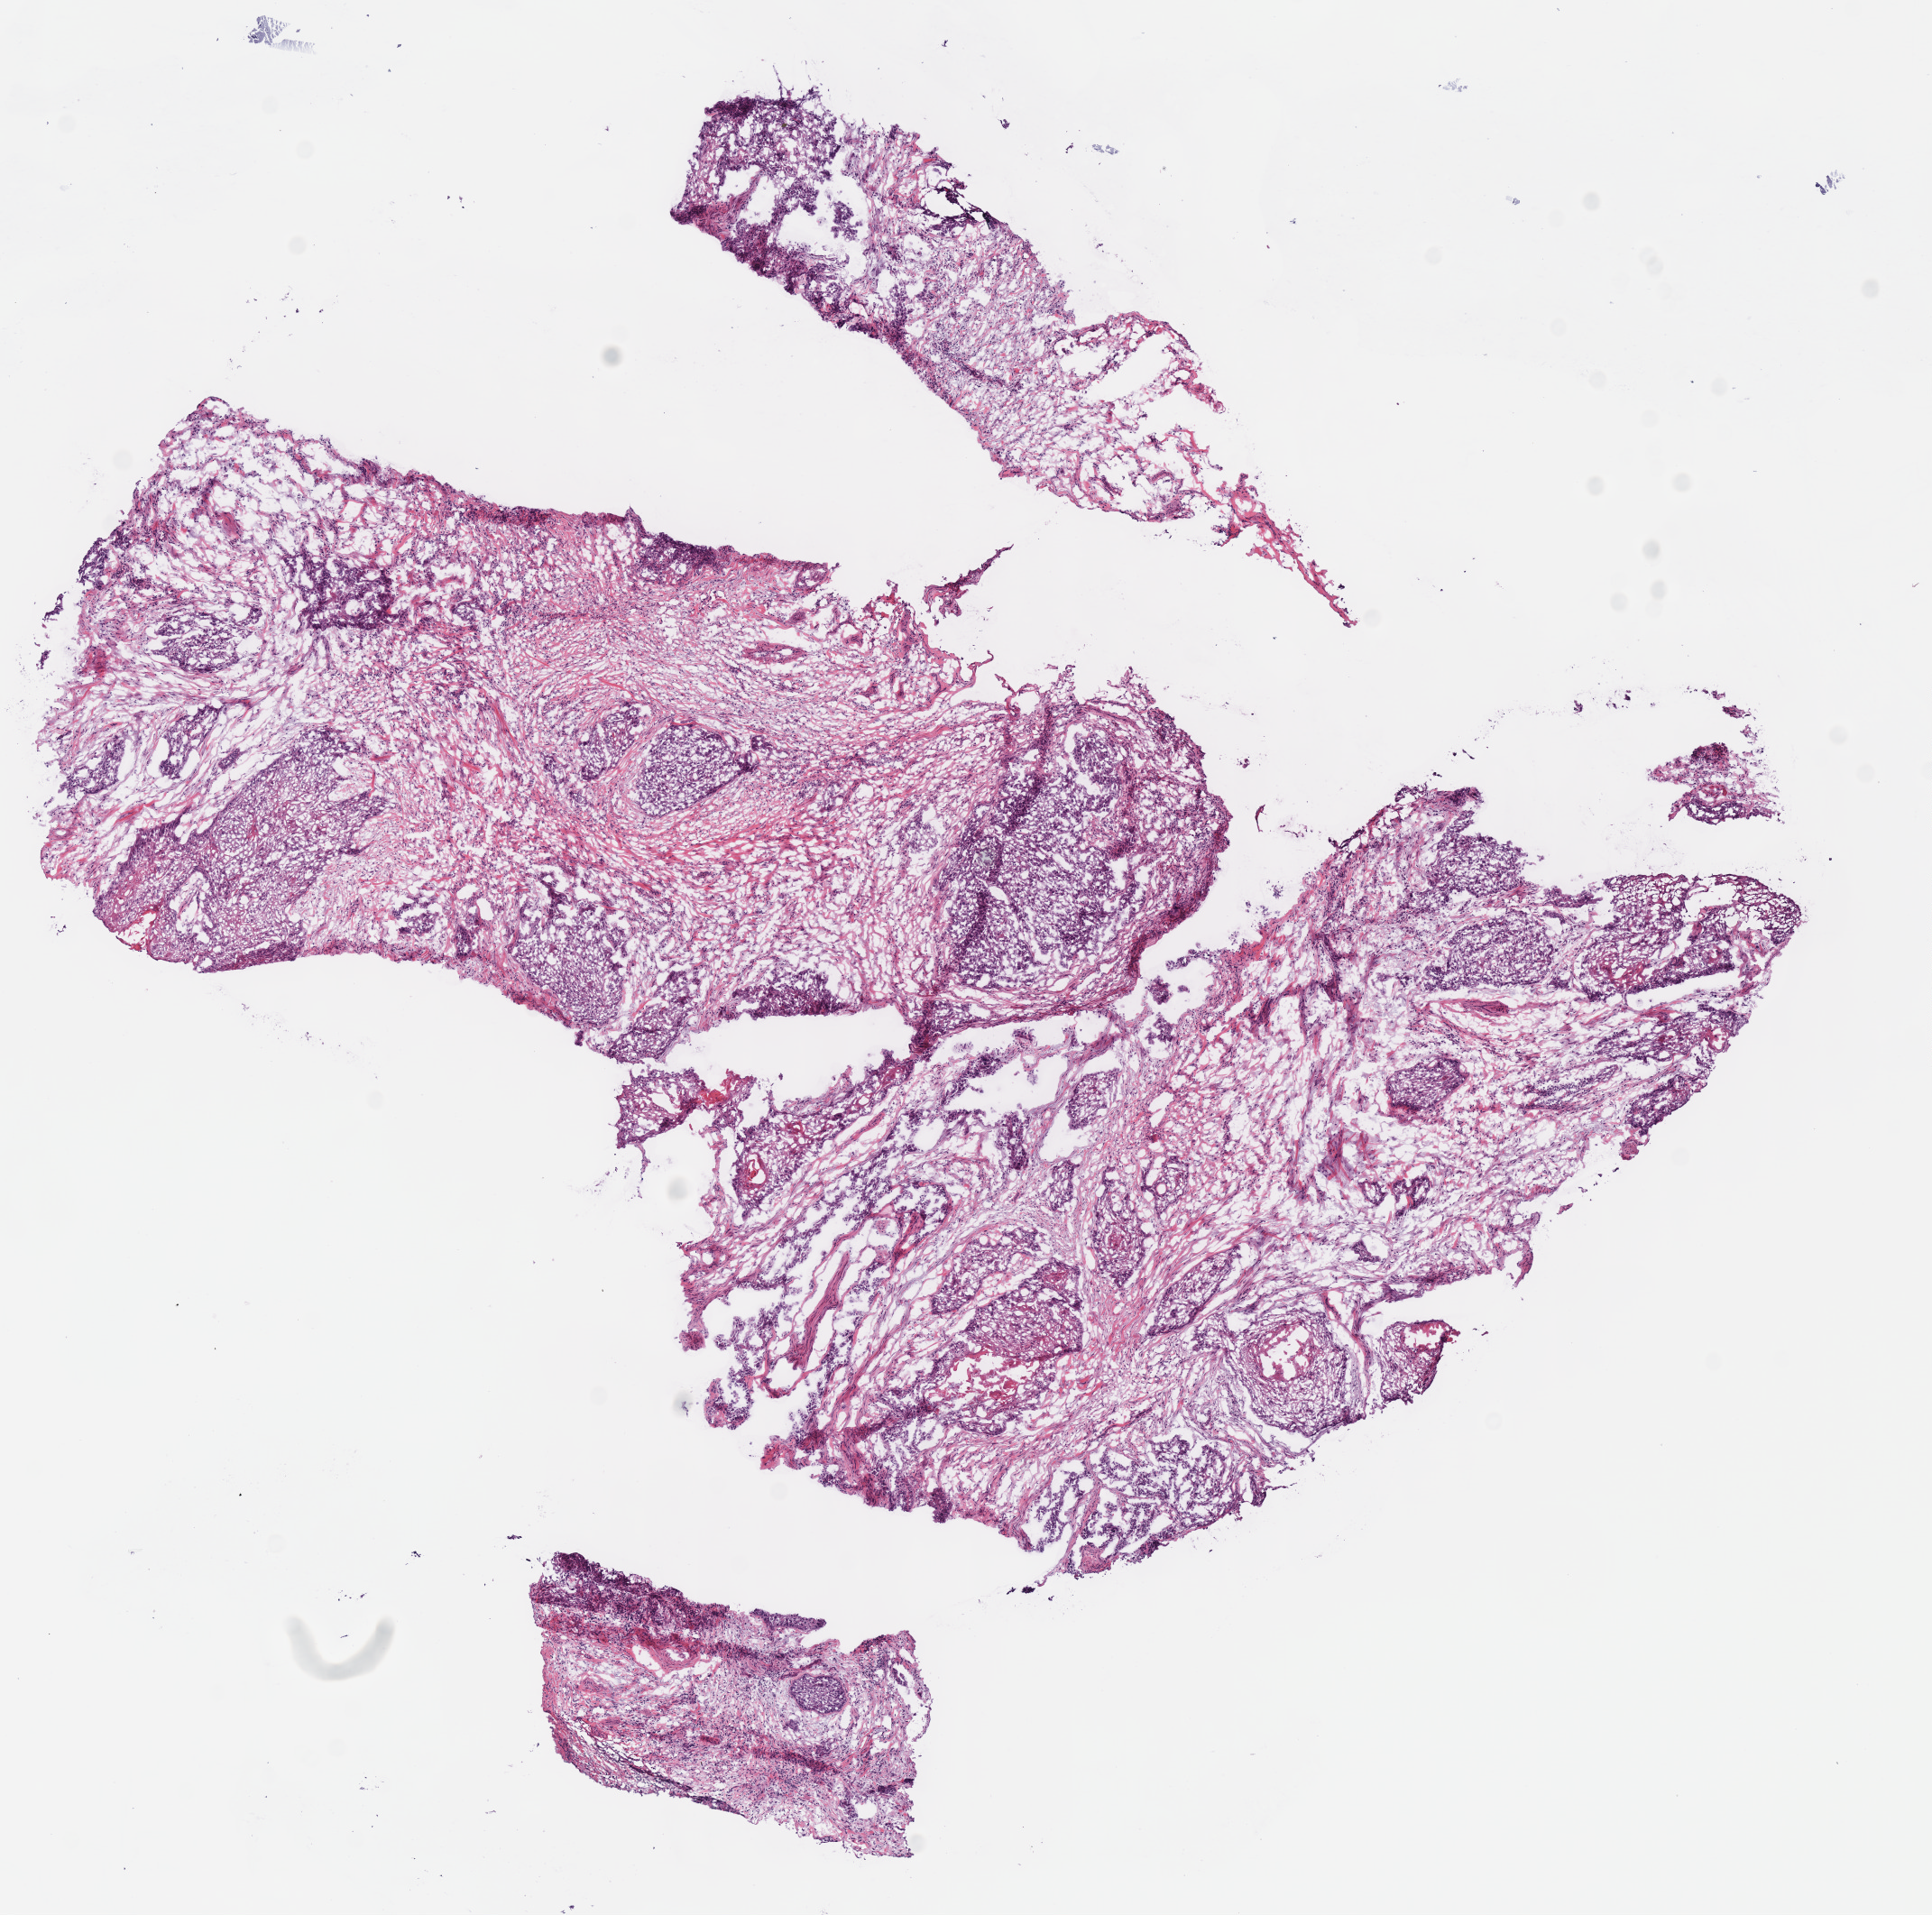
Whole-slide histology image, H&E-stained — low-resolution overview of the scanned area, about 8.4 x 8.4 mm; frozen section; sample: primary tumour, head and neck. Patient: female, age at initial diagnosis 67 years.
Diagnosis: Squamous cell carcinoma, NOS (floor of mouth, NOS).